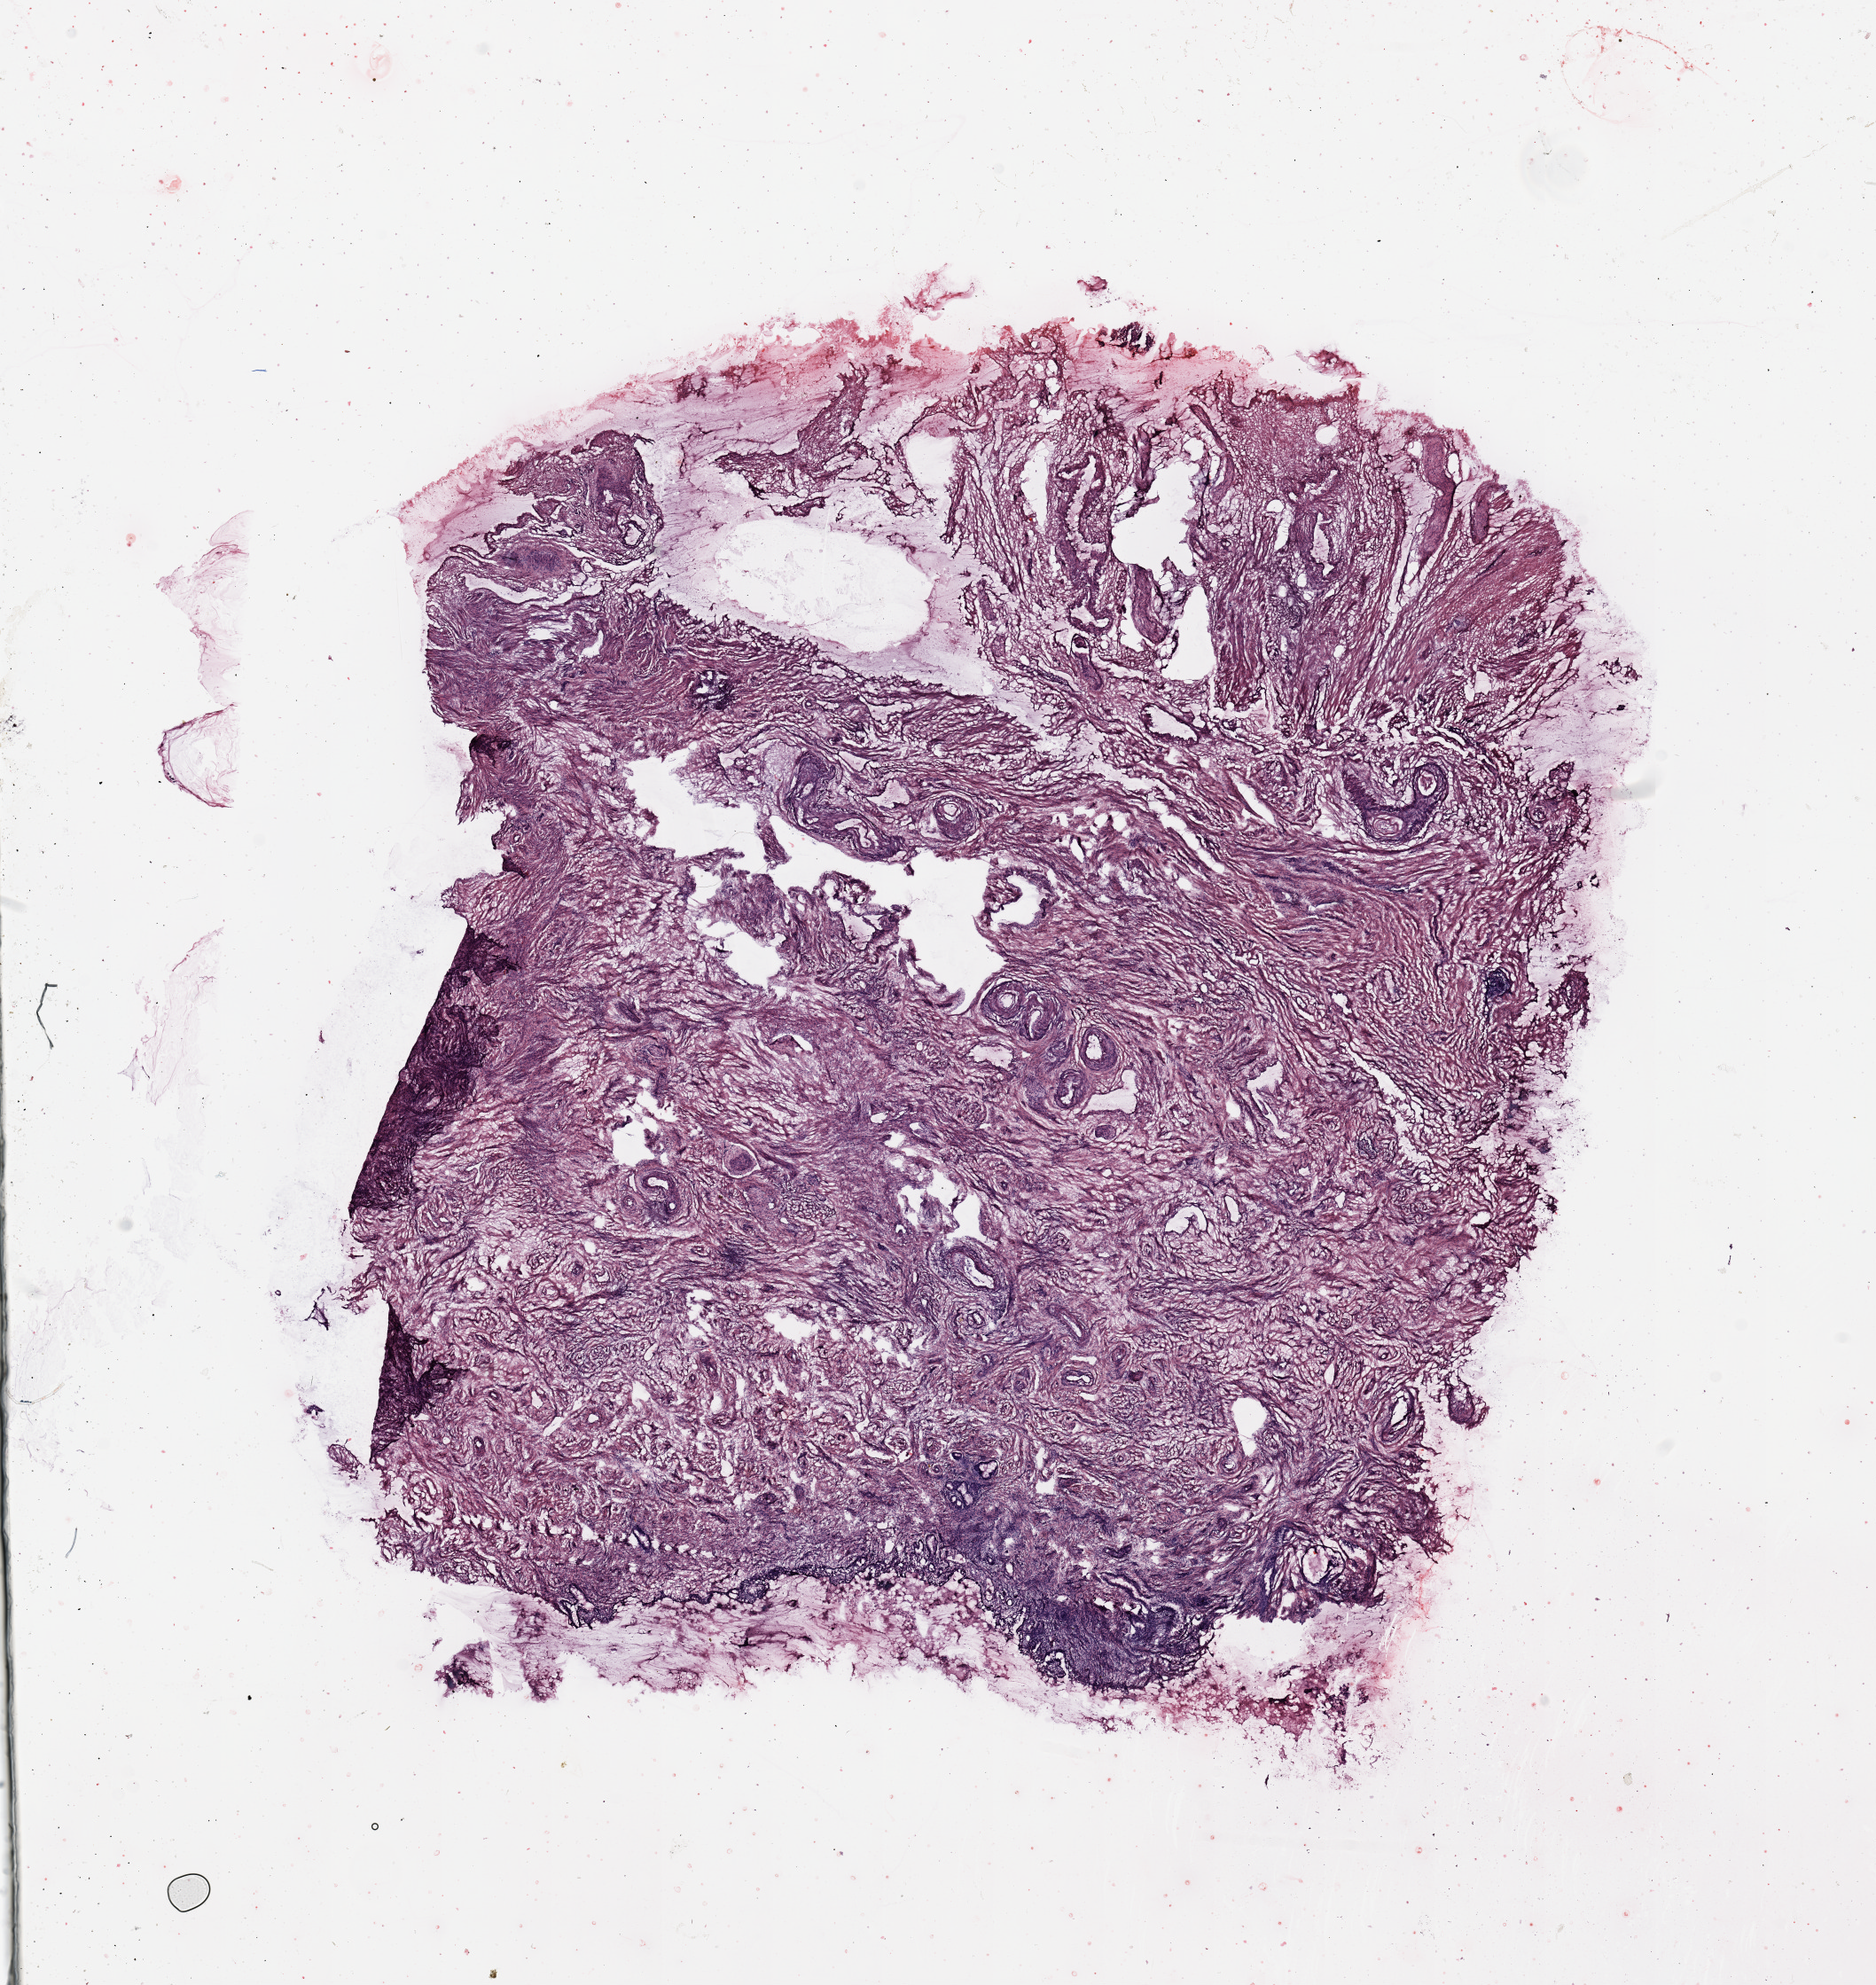
H&E whole-slide image — low-resolution overview of the scanned area, about 16.7 x 17.7 mm (acquisition: 20x scan); uterus, normal (non-tumour) tissue. Patient: female, age 64 years.
• this section: normal (non-tumour) tissue from the same patient
• patient diagnosis: Endometrioid adenocarcinoma, NOS